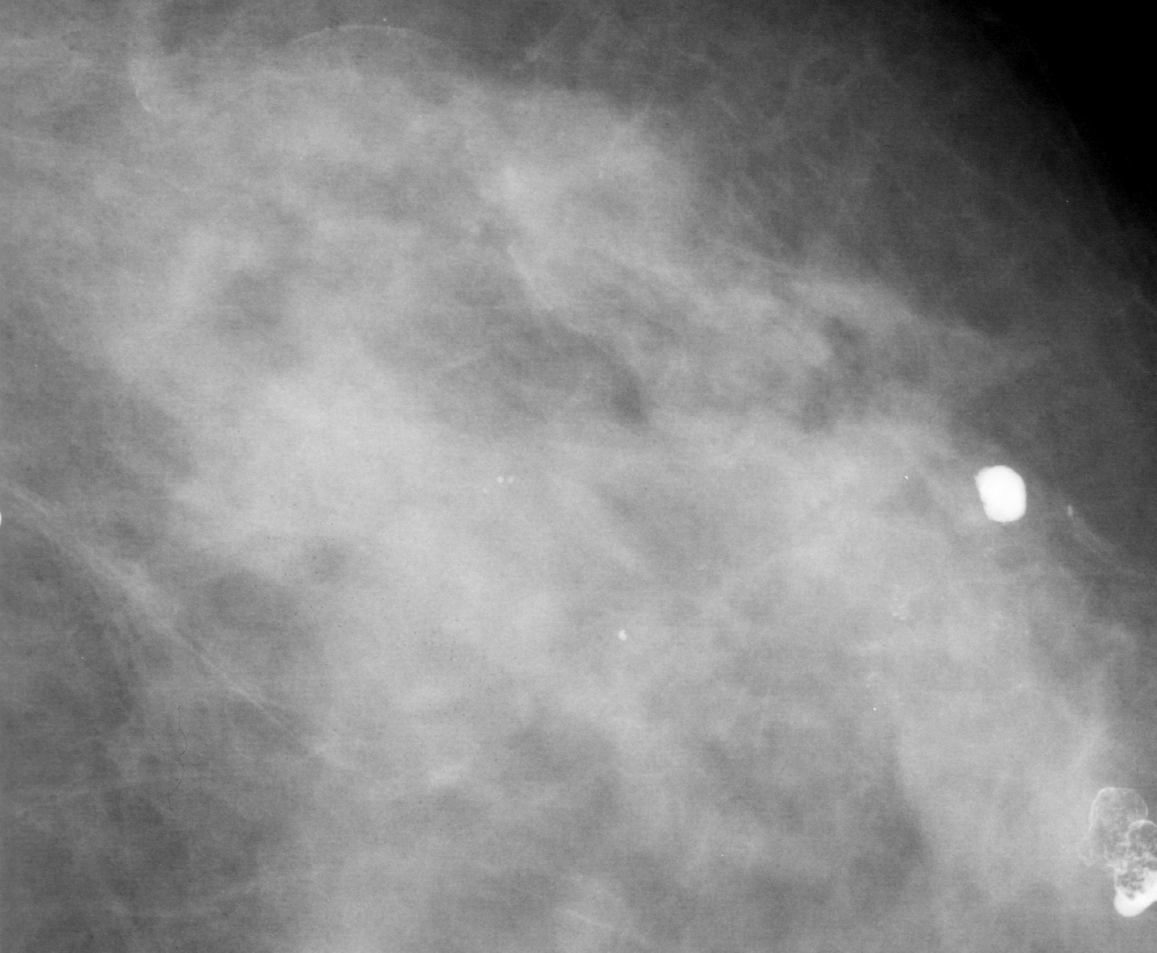
Region of interest cut from a scanned film mammogram (one marked finding); left breast; CC view.
- Marked abnormality: calcifications, morphology punctate, distribution segmental; BI-RADS assessment category 4; subtlety rating 2 on a 1 (subtle) to 5 (obvious) scale; pathology result (as recorded, not read from the image): malignant.